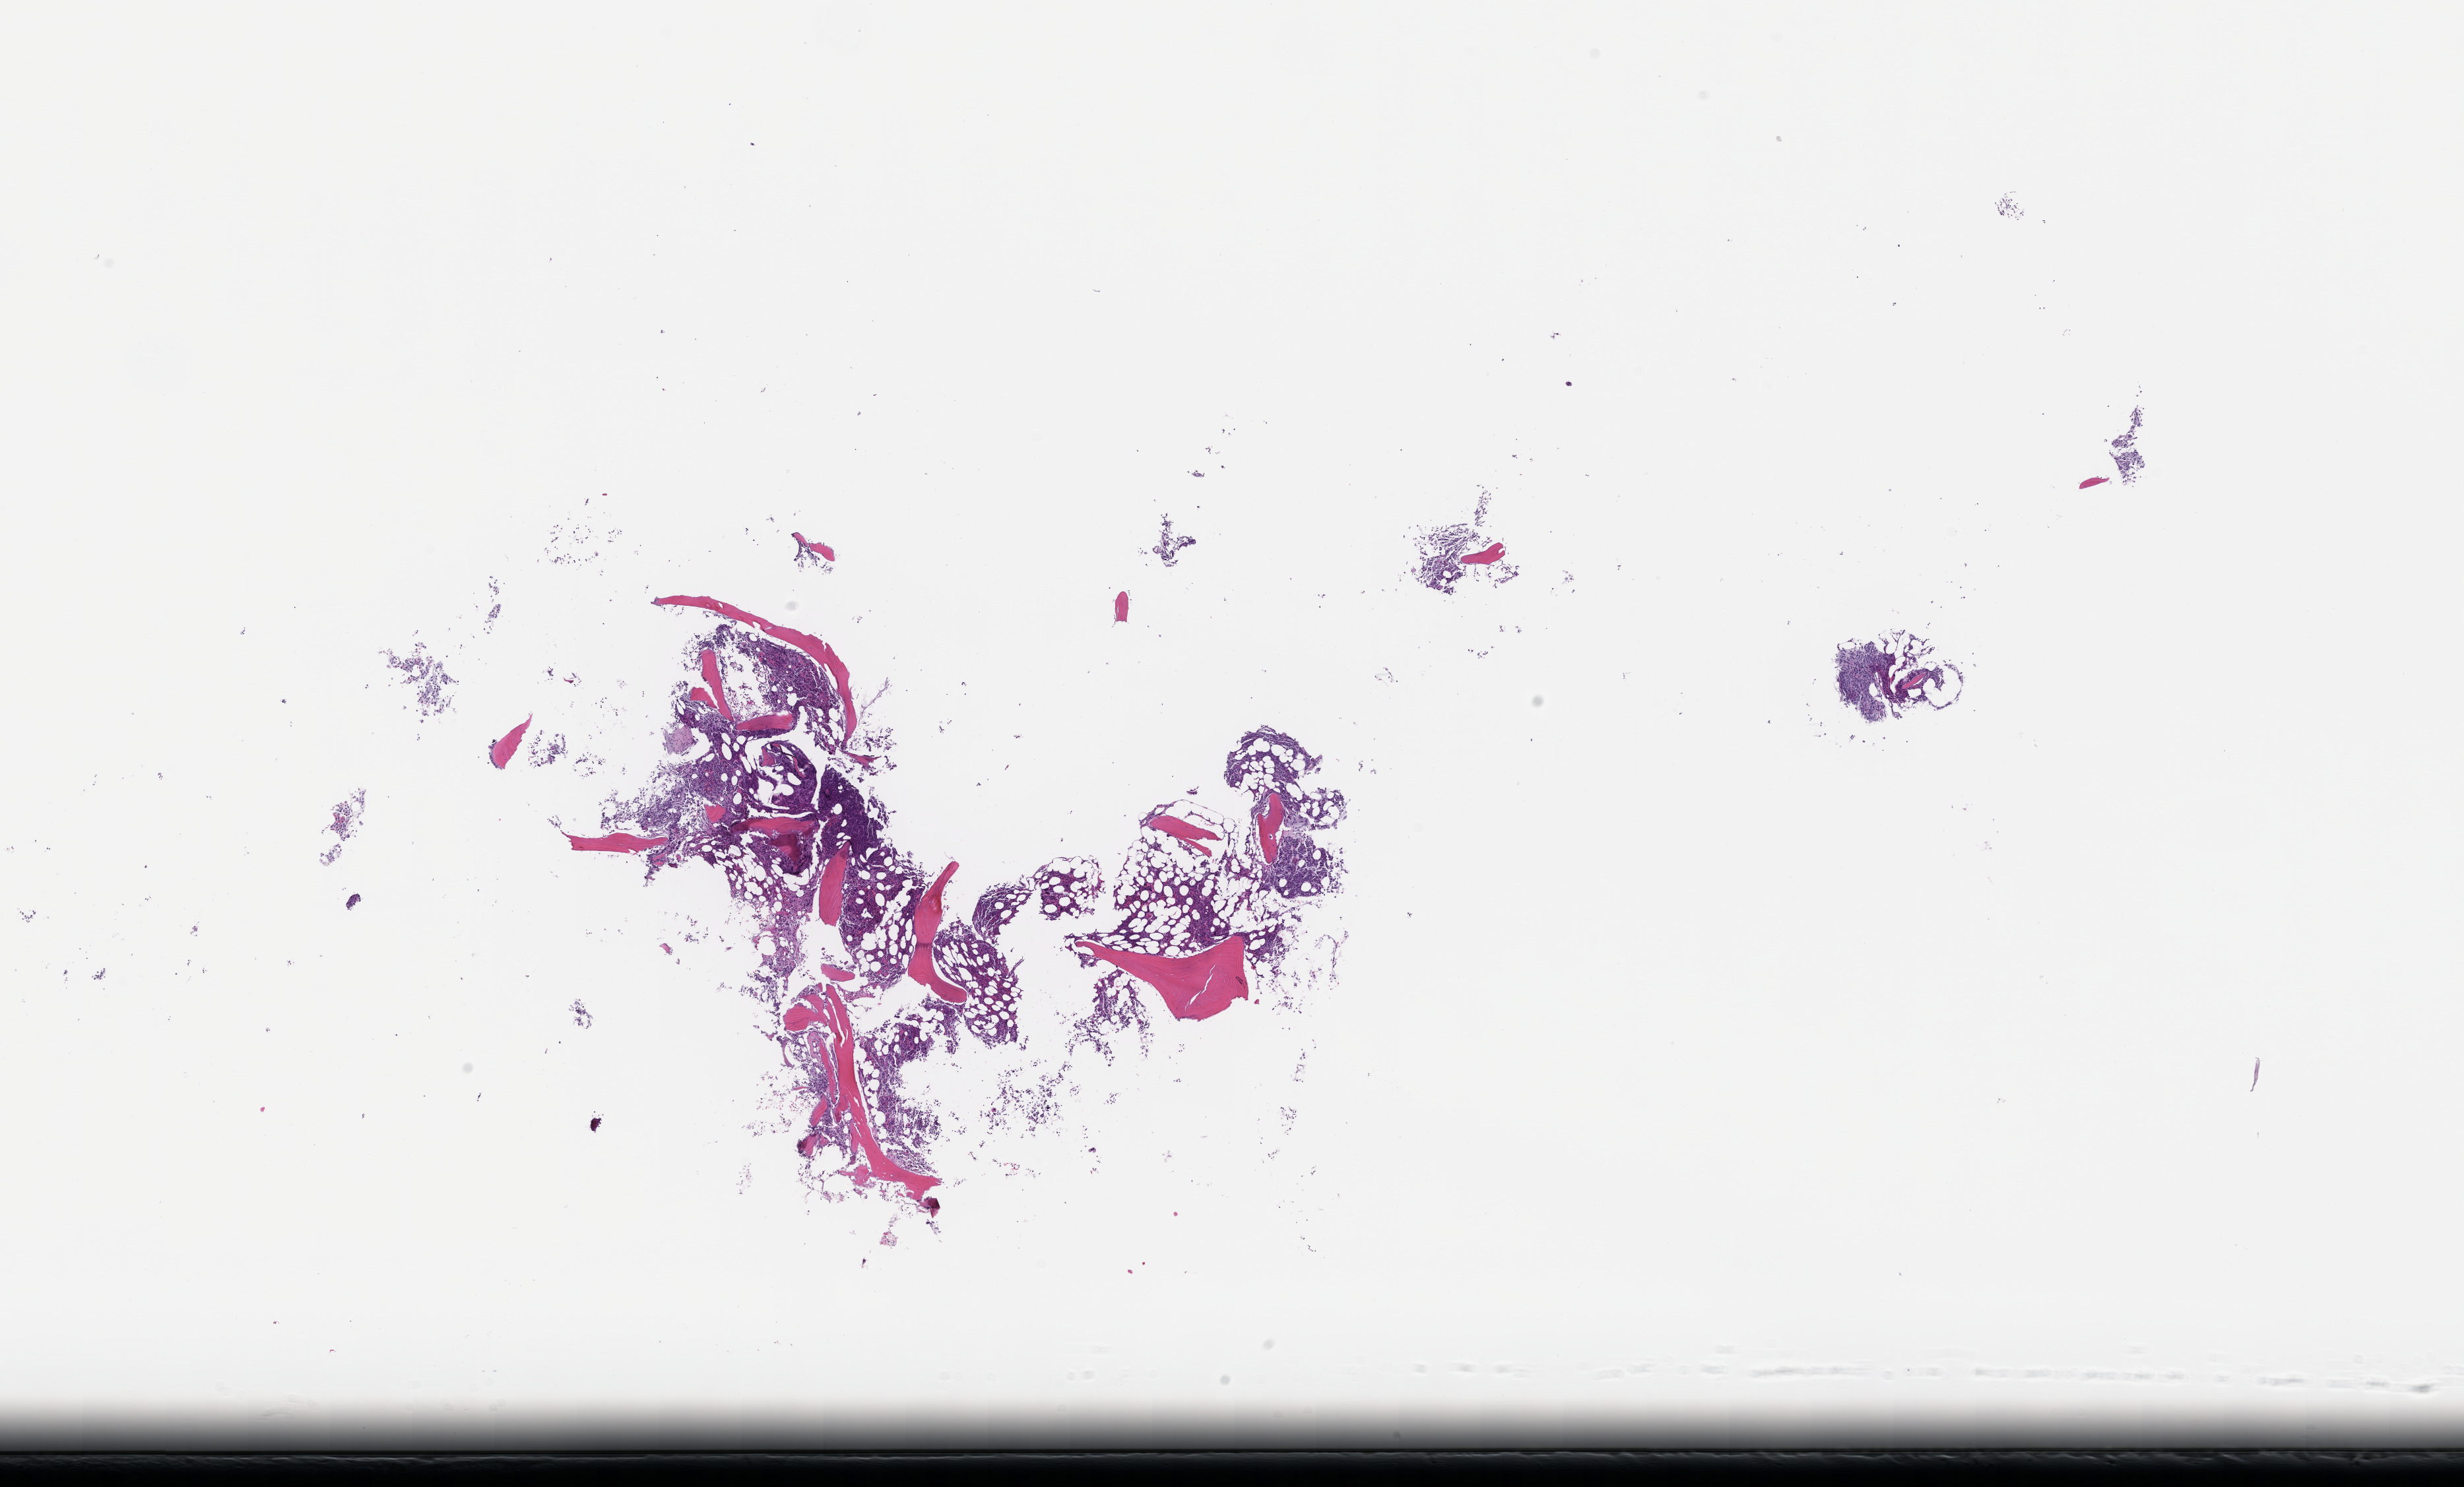
Hematoxylin and eosin (H&E) whole-slide image, low-resolution overview of the scanned area, about 15.1 x 9.1 mm. Formalin-fixed, paraffin-embedded (FFPE) tissue. Tissue site: bone marrow. Patient: female.
This section: primary tumour tissue. Diagnosis: Plasma Cell Myeloma.